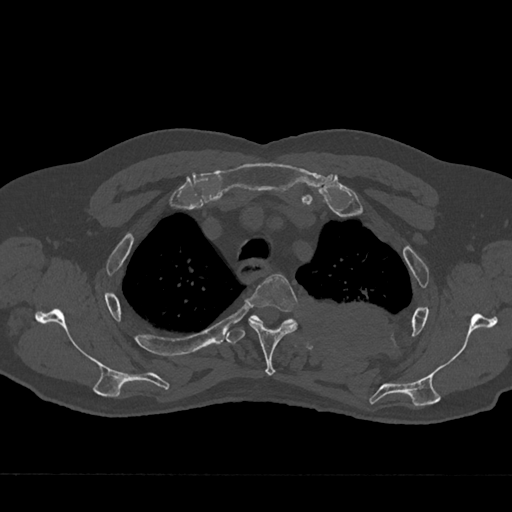
CT including the spine, one axial slice; slice 555 of 797 in the series (ordered by position); reconstruction kernel Br40s/3; bone window (W 1800 / L 400 HU); 0.5 mm slice thickness; 512 × 512 image matrix. Male patient, age 75 years. Case-level facts recorded for this patient, not image findings: primary cancer: renal; vertebrae with lytic lesions (as recorded): T4.
Structures marked on this image (semi-automatically segmented with operator editing):
- T3 vertebra: bounding box [x1, y1, x2, y2] px = [248, 274, 298, 376]
- T4 vertebra: [226, 314, 296, 344]